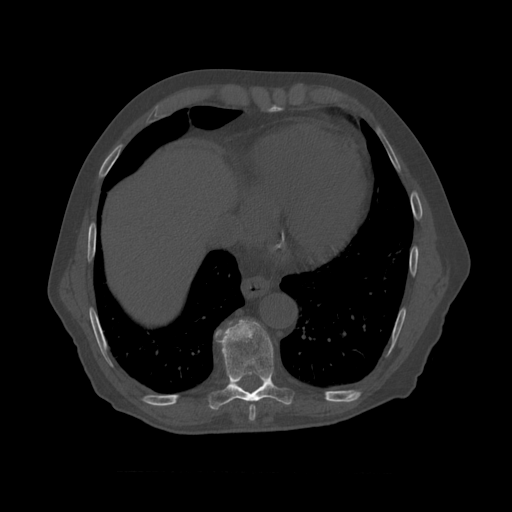
CT including the spine, one axial slice; position 446 of 450 along the scan axis; bone window (W 1800 / L 400 HU); 1.25 mm slice thickness; 512 × 512 image matrix, field of view 405 × 405 mm. Patient age 75 years. Case-level facts recorded for this patient, not image findings: primary cancer: prostate.
Outlined on this slice (semi-automatically segmented with operator editing):
- T8 vertebra: bounding box [x1, y1, x2, y2] px = [215, 319, 293, 411]